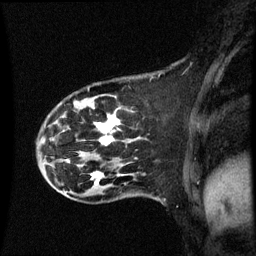
Breast MRI (dynamic contrast-enhanced), one sagittal slice; slice 17 of 60 in the series (ordered by position); dynamic contrast-enhanced series, image 2 of 3 at this slice position (ordered by acquisition); 1.5 T; TE 4.2 ms, TR 8.9 ms; 2 mm slice thickness; 256 × 256 image matrix. Patient: female, 44 years. From the clinical record (not read from this slice): setting: breast cancer imaged before/during neoadjuvant chemotherapy; receptor status: HR-positive, HER2-negative.
Structures marked on this image (semi-automatic segmentation, software-assisted and operator-edited):
- analysis volume of interest (the breast-tissue region the enhancement analysis was run in; not a lesion): box from (x=43, y=88) to (x=142, y=189) px
- tumour enhancement mask (voxels above the 70 % enhancement threshold inside the analysis volume of interest): (x=91, y=116)–(x=120, y=185)